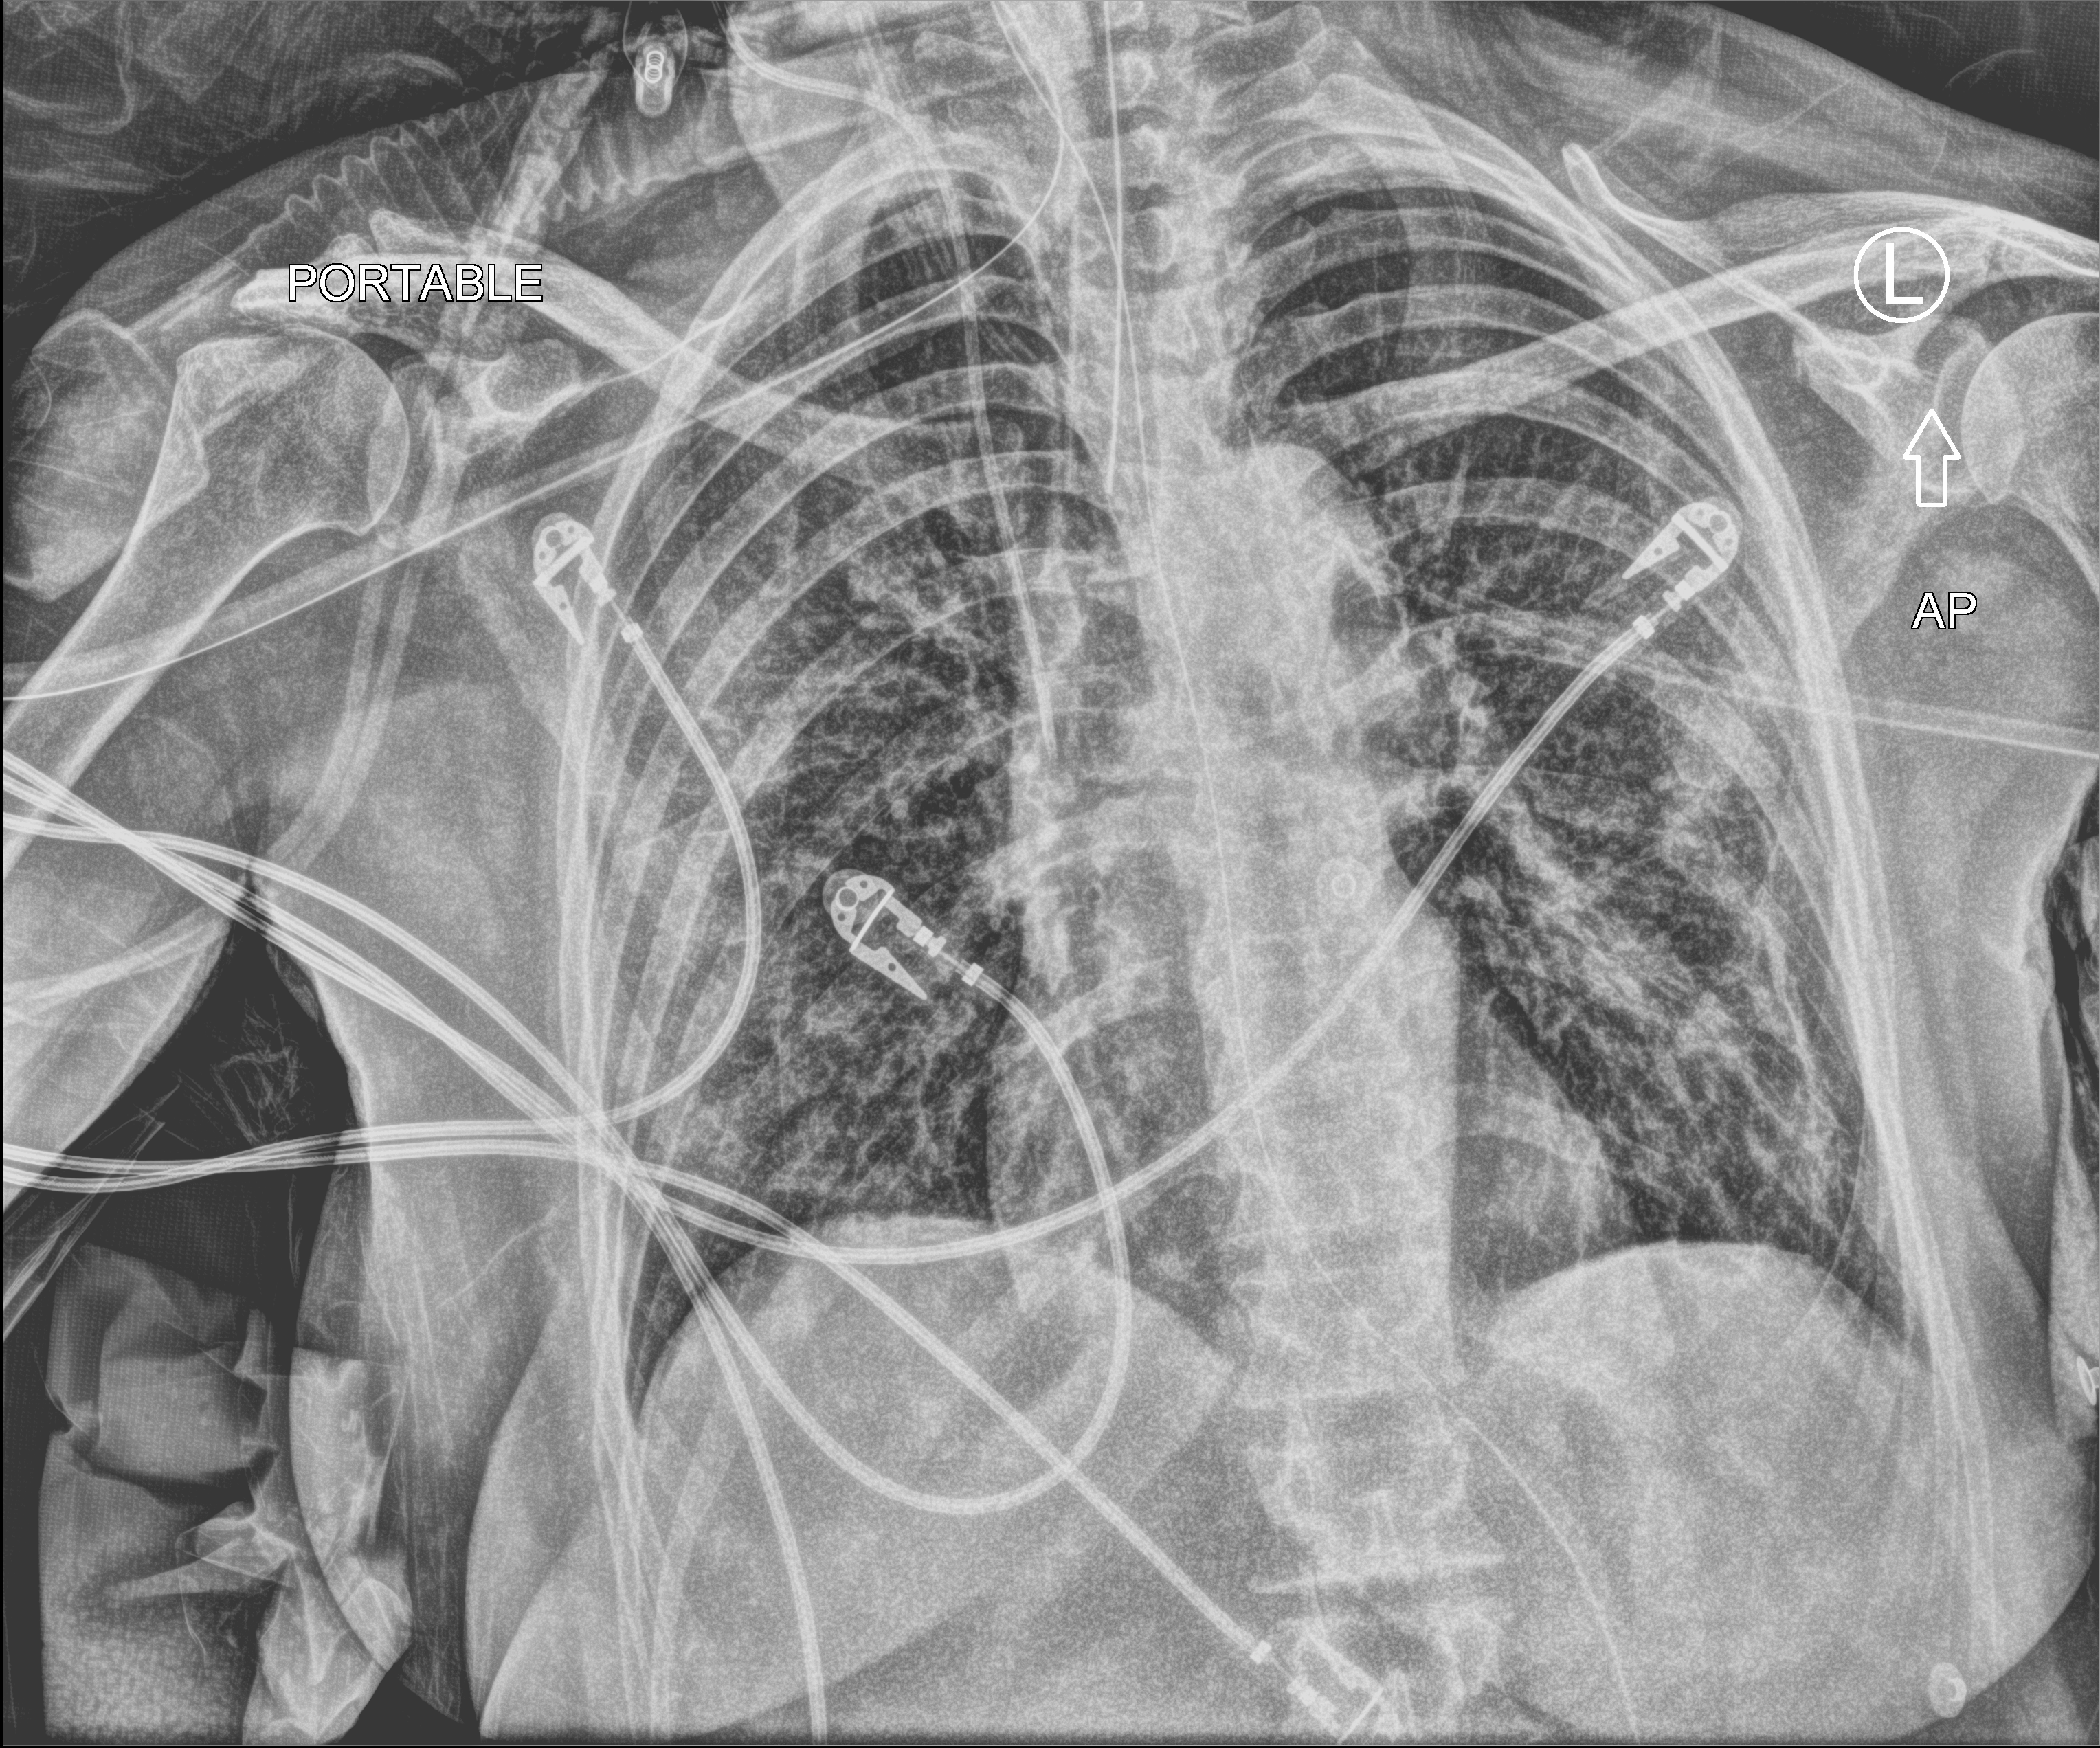
Portable chest radiograph; anteroposterior (AP) projection. Female patient hospitalised with COVID-19, age 60–74 years.
Hospital-stay facts (about this admission, not read from this image; timing relative to this image not recorded):
- admitted to intensive care during this hospital stay: yes
- length of hospital stay: 18 days